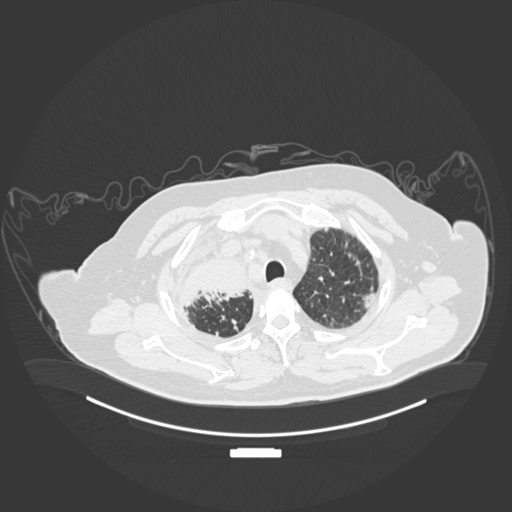
Chest CT, one axial slice. Position 157 of 201 along the scan axis. Reconstruction kernel B30f. Lung window (W 1500 / L -600 HU). 1 mm slice thickness. 512 × 512 image matrix. Patient: male, 69 years. From the clinical record (not read from this slice): clinical TNM (as recorded): T4 N3 M1.
Outlined on this slice (rectangle marked by the reading radiologist):
- lung tumour (recorded histology: adenocarcinoma): bounding box (x1, y1, x2, y2) in pixels: (178, 260, 252, 309)